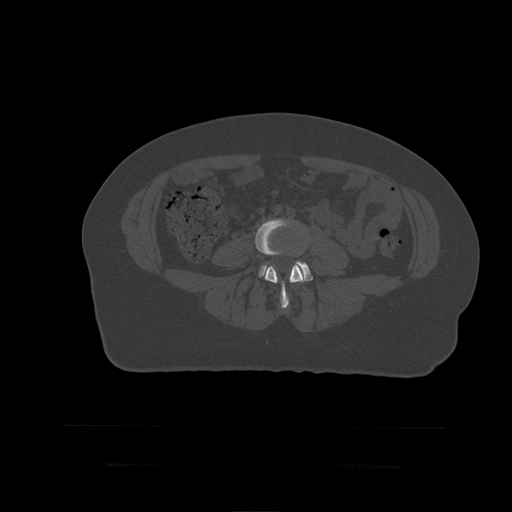
CT including the spine, one axial slice; slice 88 of 399 in the series (ordered by position); reconstruction kernel STANDARD; bone window (W 1800 / L 400 HU); 1.25 mm slice thickness; 512 × 512 image matrix, field of view 450 × 450 mm. Patient age 41 years. Case-level facts recorded for this patient, not image findings: primary cancer: breast.
Outlined on this slice (semi-automatically segmented with operator editing):
- L4 vertebra: bounding box <255,218,307,309> (left, top, right, bottom; pixels)
- L5 vertebra: <259,261,313,281>